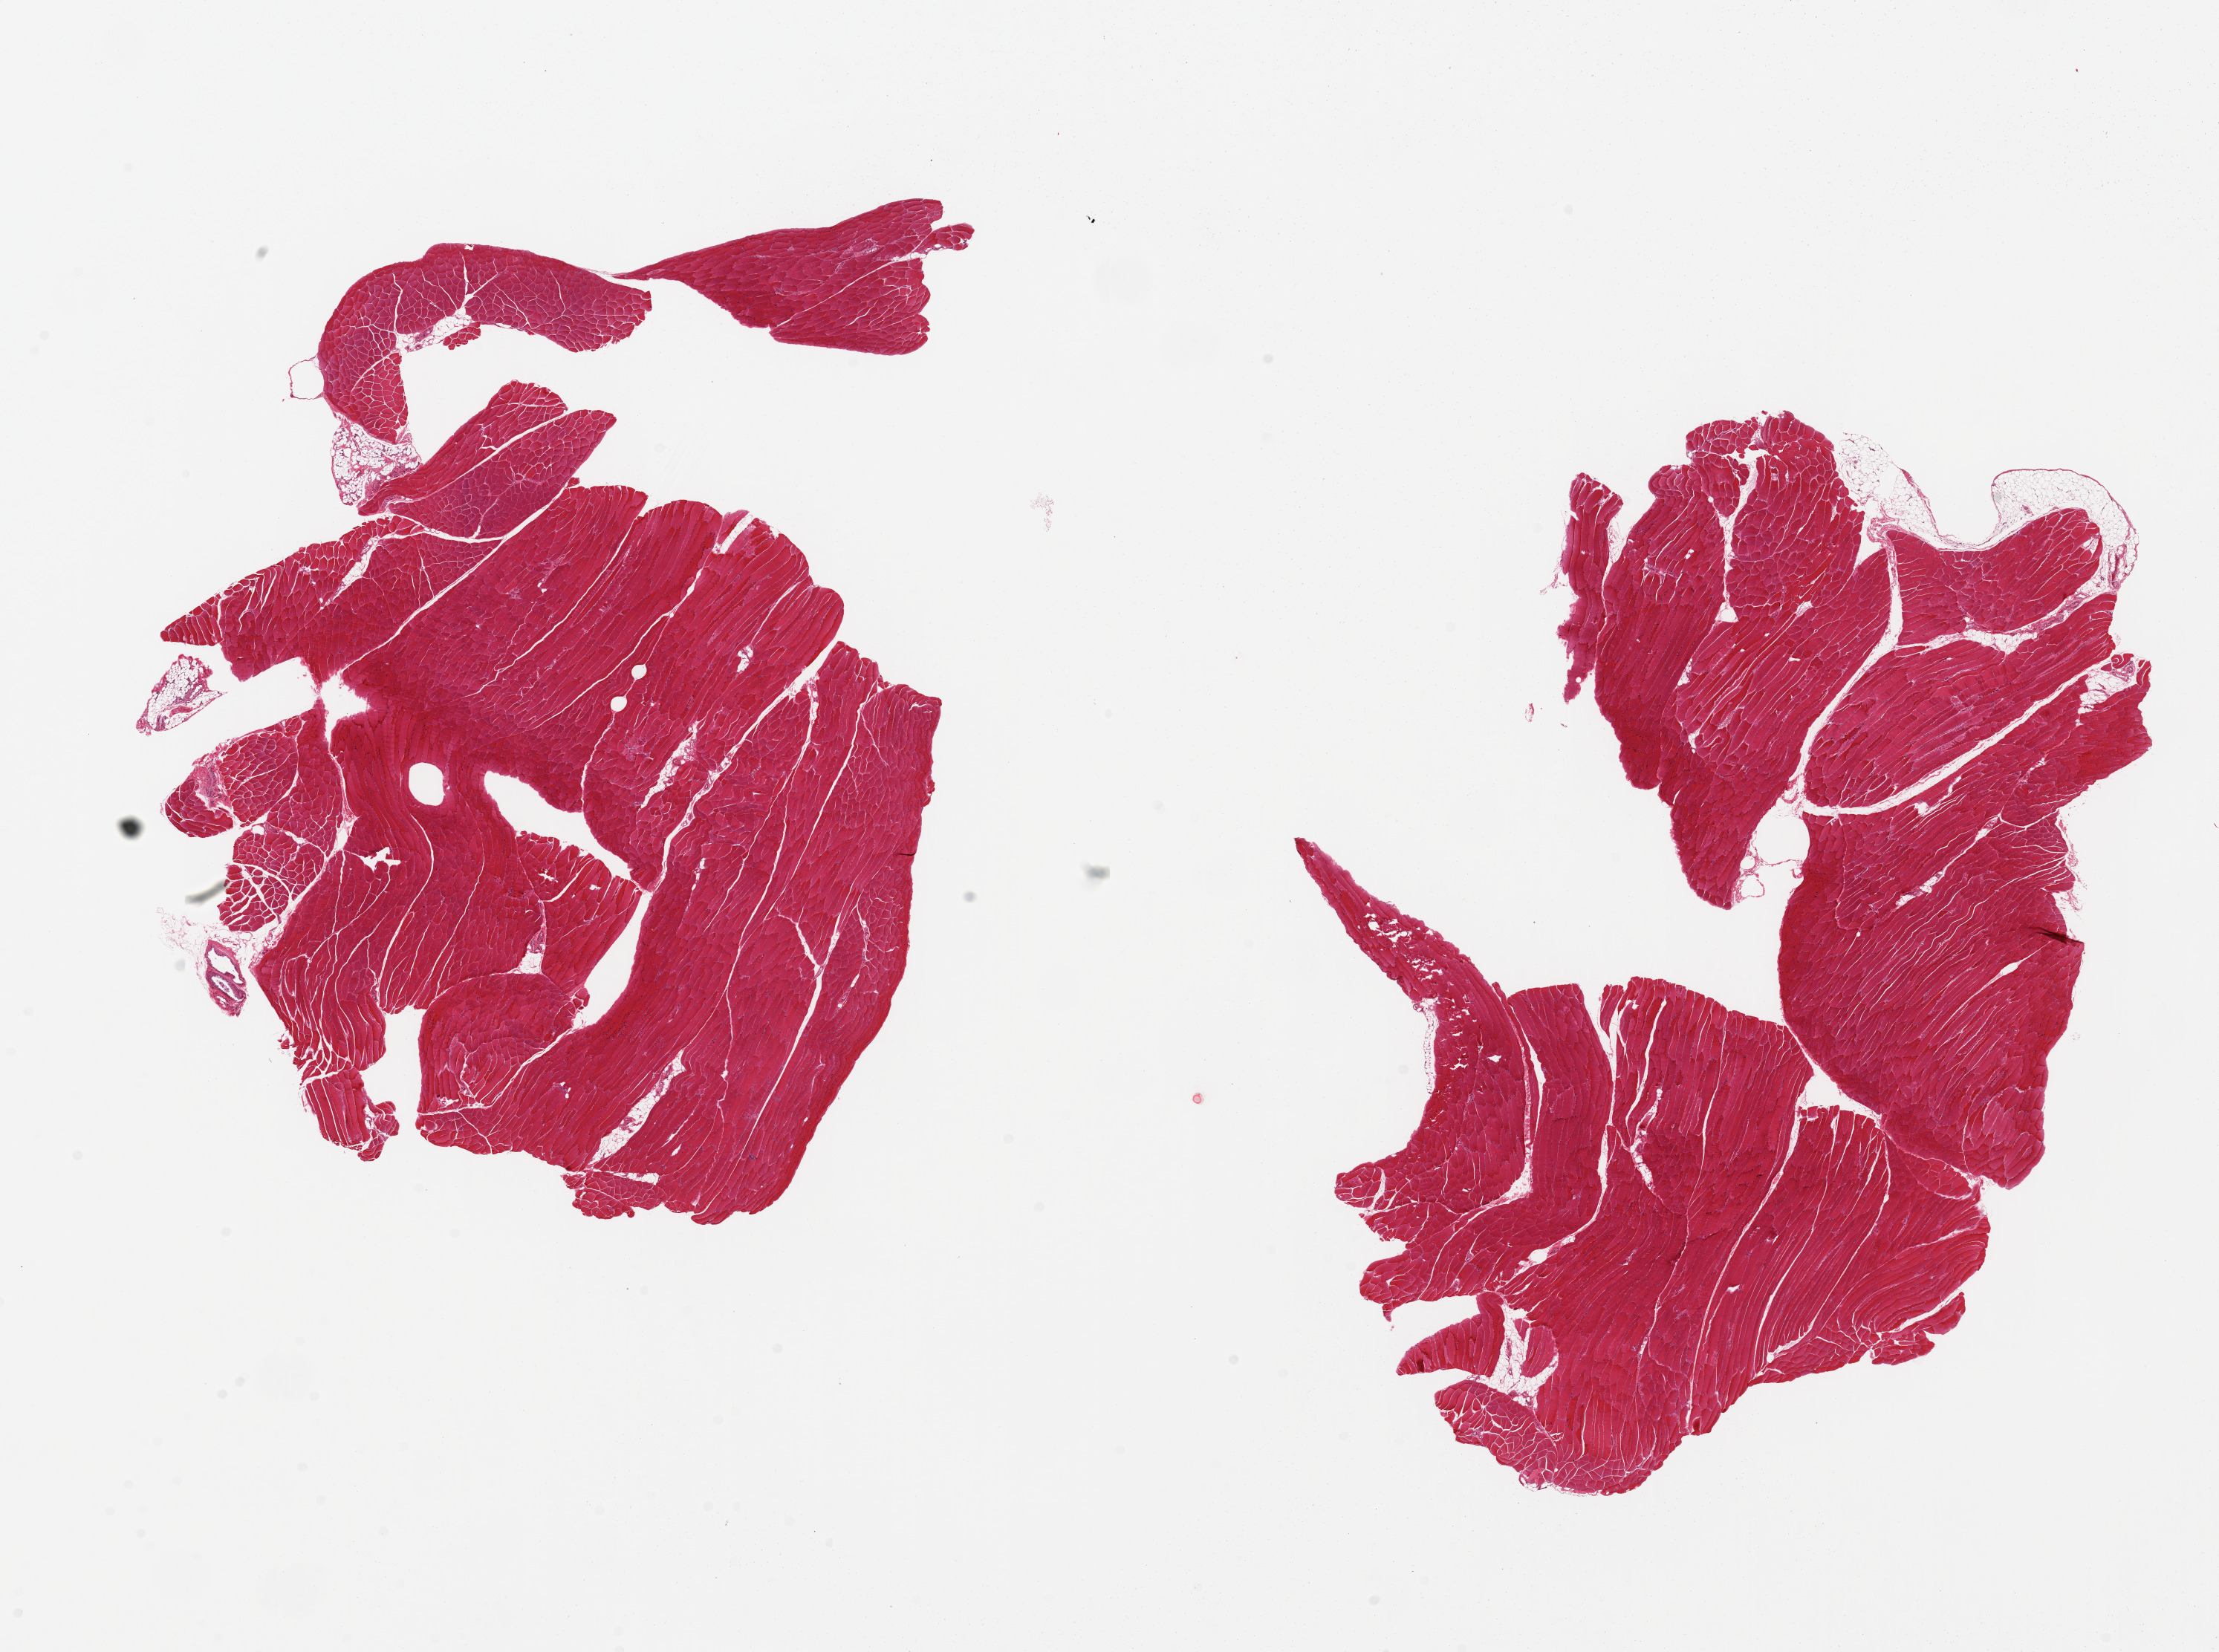
Digitized hematoxylin and eosin (H&E)-stained section, shown as a low-resolution overview of the whole scanned area (about 23.6 x 17.6 mm); PAXgene-fixed, paraffin-embedded tissue; target tissue: skeletal muscle; tissue donor sample. Female donor.
Pathologist's review note for this sample: 2 pieces, <1% interstitial fat; trace adherent fat.